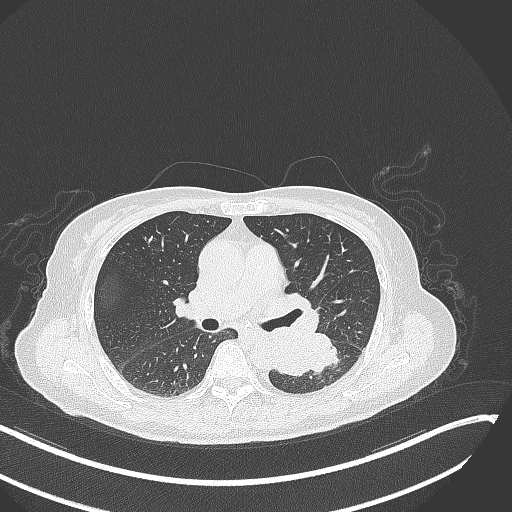
Chest CT, one axial slice; slice 161 of 342 in the series (ordered by position); reconstruction kernel B70f; lung window (W 1500 / L -600 HU); 512 × 512 image matrix, field of view 400 × 400 mm. Patient: female, 64 years. Case-level facts recorded for this patient, not image findings: clinical TNM (as recorded): T3 N1 M1; histopathological grade: G3.
Structures marked on this image (rectangle marked by the reading radiologist):
- lung tumour (recorded histology: small cell carcinoma): bounding box [x1, y1, x2, y2] px = [274, 332, 341, 381]